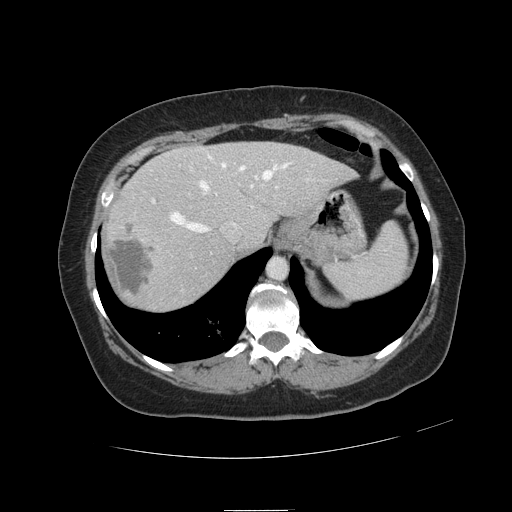
Contrast-enhanced abdominal CT, one axial slice. 120 kVp. Soft-tissue window (W 400 / L 40 HU). 2.5 mm slice thickness. 512 × 512 image matrix, field of view 400 × 400 mm. Female patient, age 52 years. From the clinical record (not read from this slice): diagnosis: colorectal cancer liver metastases, imaged before liver resection; multiple liver metastases: yes; largest metastasis: 6.3 cm; chemotherapy before resection: yes.
Structures marked on this image (outlined manually by an expert reader):
- hepatic veins: bounding box (x1, y1, x2, y2) in pixels: (171, 155, 289, 233)
- liver: (105, 143, 353, 311)
- planned liver remnant (the part of the liver to remain after resection): (169, 143, 353, 246)
- portal vein (with intrahepatic branches): (152, 186, 279, 203)
- liver metastasis: (109, 232, 155, 296)